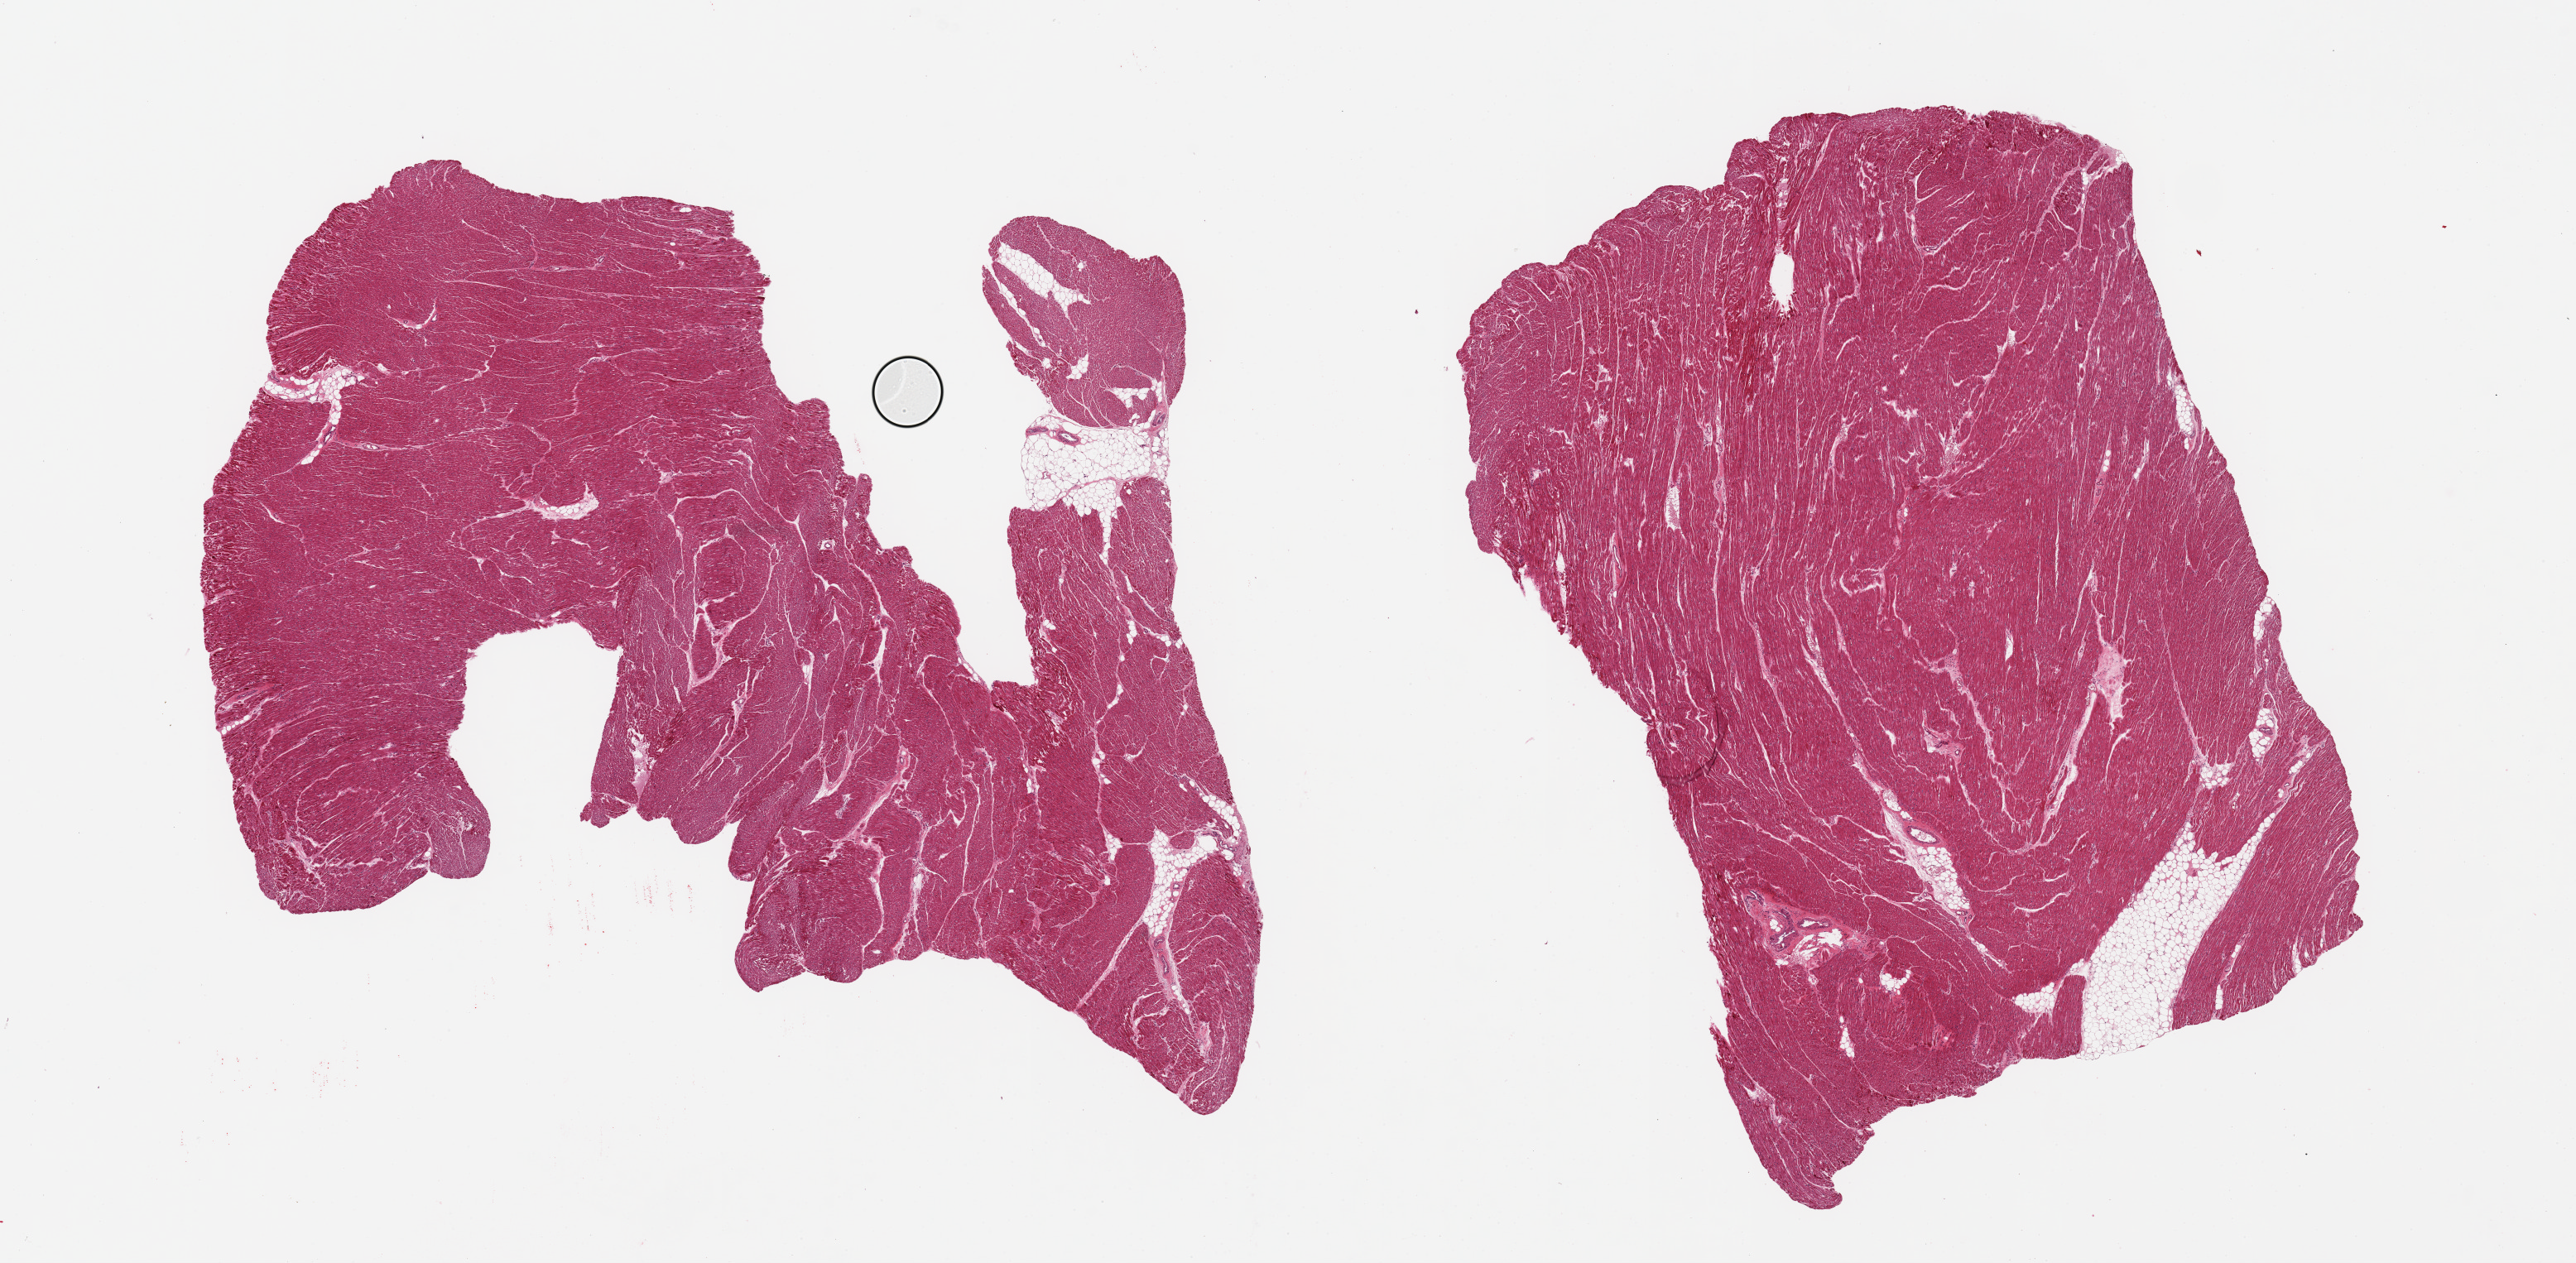
Whole-slide image, haematoxylin and eosin stain, a low-resolution overview of the entire scanned area, about 24.6 x 12.1 mm (slide scanned at 20x), PAXgene-fixed, paraffin-embedded tissue, sampled site (target tissue): heart, donor tissue sample. Donor sex: male.
Reviewer comment on this tissue sample: 2 pieces, each with ~5% fat; contraction bands seen.